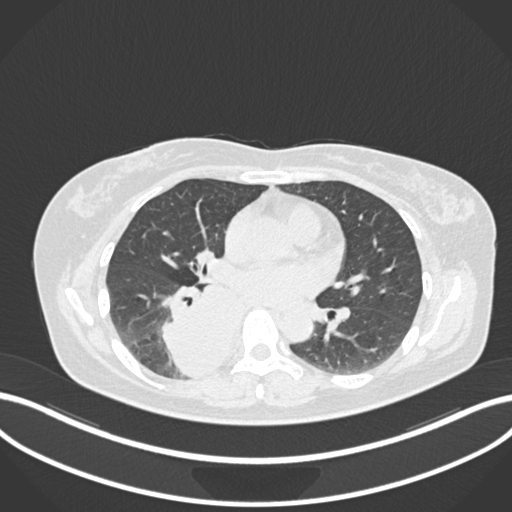
Chest CT, one axial slice; slice 584 of 677 in the series (ordered by position); lung window (W 1500 / L -600 HU); 1 mm slice thickness; 512 × 512 image matrix, field of view 400 × 400 mm. Female patient, age 54 years. From the clinical record (not read from this slice): clinical TNM (as recorded): T4 N0 M0.
Annotated regions visible in this slice (bounding box drawn by a radiologist):
- lung tumour (recorded histology: adenocarcinoma): bounding box (x1, y1, x2, y2) in pixels: (147, 278, 248, 383)